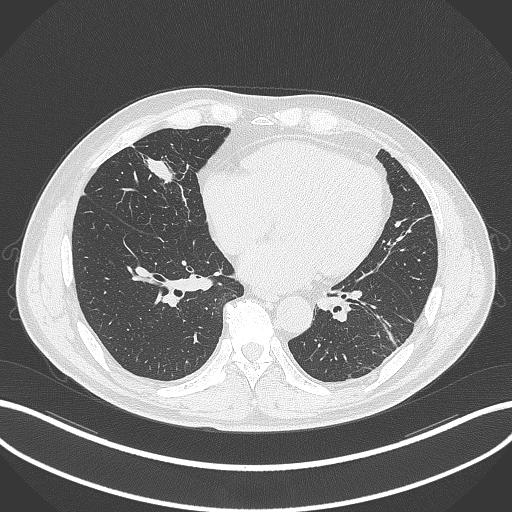
Chest CT, one axial slice. Slice 102 of 399 in the series (ordered by position). Reconstruction kernel B70f. 120 kVp. Lung window (W 1500 / L -600 HU). 512 × 512 image matrix. Male patient, age 59 years. Case-level facts recorded for this patient, not image findings: clinical TNM (as recorded): T2a N1 M0.
Outlined on this slice (bounding box drawn by a radiologist):
- lung tumour (recorded histology: adenocarcinoma): bounding box <142,153,183,187> (left, top, right, bottom; pixels)